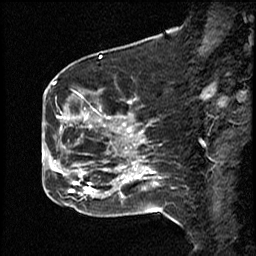
Breast MRI (dynamic contrast-enhanced), one sagittal slice. Dynamic contrast-enhanced study with each time point stored as its own series, time point 2 of 4 at this slice position (early post-contrast, ordered by acquisition time). 1.5 T. TE 4.2 ms, TR 18.5 ms. 3 mm slice thickness. 256 × 256 image matrix. Patient: female, 44 years. Case-level facts recorded for this patient, not image findings: setting: breast cancer imaged before/during neoadjuvant chemotherapy; receptor status: HR-positive, HER2-negative.
Annotated regions visible in this slice (semi-automatically segmented with operator editing):
- analysis volume of interest (the breast-tissue region the enhancement analysis was run in; not a lesion): bounding box [x1, y1, x2, y2] px = [59, 91, 114, 206]
- tumour enhancement mask (voxels above the 100 % enhancement threshold inside the analysis volume of interest): [63, 117, 110, 196]